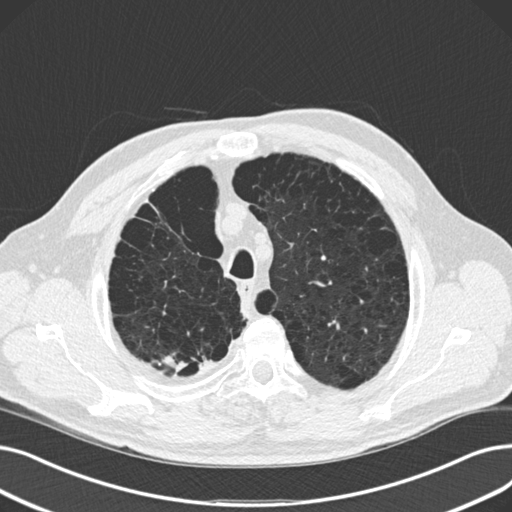
Low-dose screening chest CT, one axial slice. Reconstruction kernel B30f. 120 kVp. Lung window (W 1500 / L -600 HU). 512 × 512 image matrix.
Outlined on this slice (manually delineated by an expert):
- lesion 2 (tumor, upper lobe of right lung): bounding box [x1, y1, x2, y2] px = [164, 356, 187, 373]